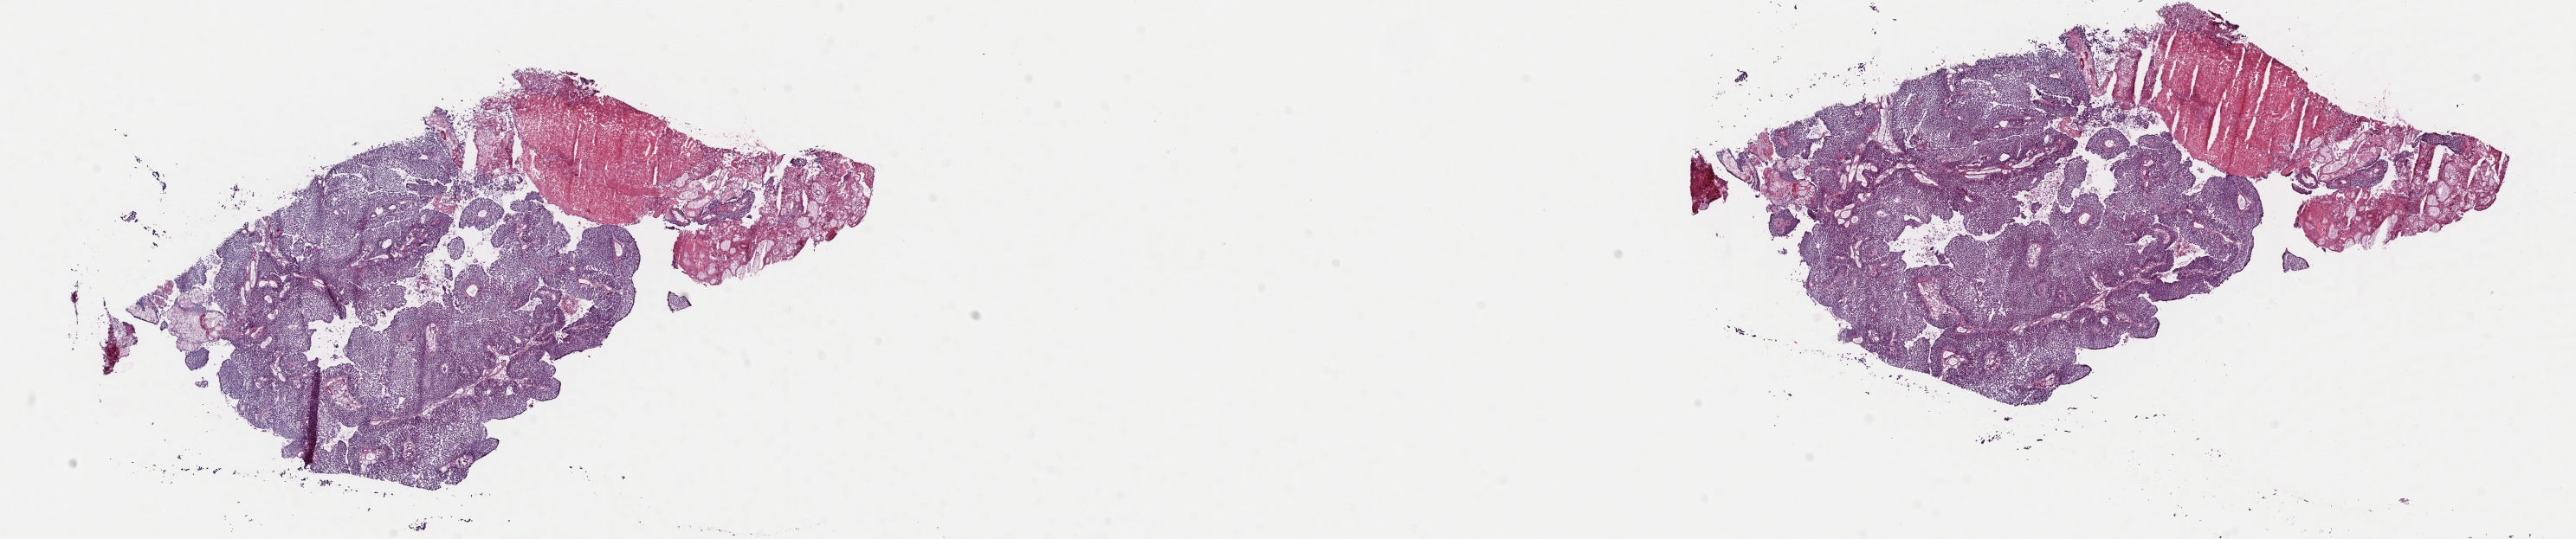
Whole-slide histology image, H&E-stained, low-resolution overview of the scanned area, about 23.5 x 4.9 mm (from a 40x scan), frozen section from the top of the tissue portion, sample: primary tumour, bladder. Patient: male, age at initial diagnosis 61 years. Histologic grade: high grade. Slide review estimates, as recorded: tumour cells 80%, tumour nuclei 80%, normal cells 0%, stromal cells 0%, necrosis 20%. Inflammatory infiltration, as recorded: lymphocyte infiltration 2%, monocyte infiltration 0%, neutrophil infiltration 1%.
AJCC pathologic stage: II (6th edition). Diagnosis: Transitional cell carcinoma (lateral wall of bladder). TNM: T2b N0 M0. Lymph nodes positive (case pathology): 0 of 16 examined.